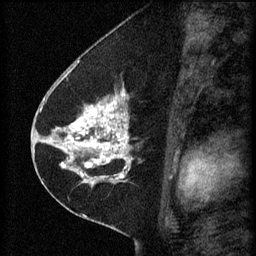
Breast MRI (dynamic contrast-enhanced), one sagittal slice. Slice 29 of 60 in the series (ordered by position). 3 images stored at this slice position (order not interpretable as contrast timing). 1.5 T. TE 4.2 ms, TR 8.2 ms. 256 × 256 image matrix, field of view 180 × 180 mm. Patient: female, 41 years.
Structures marked on this image (semi-automatic segmentation, software-assisted and operator-edited):
- analysis volume of interest (the breast-tissue region the enhancement analysis was run in; not a lesion): bounding box (x1, y1, x2, y2) in pixels: (67, 92, 165, 173)
- tumour enhancement mask (voxels above the 70 % enhancement threshold inside the analysis volume of interest): (67, 92, 131, 173)